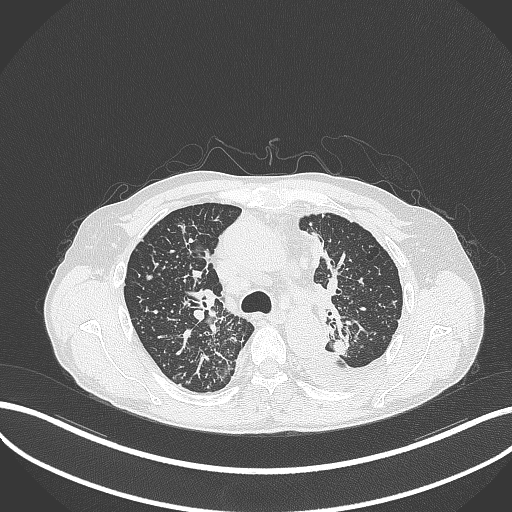
Chest CT, one axial slice. Position 248 of 325 along the scan axis. Reconstruction kernel B70f. Lung window (W 1500 / L -600 HU). 1 mm slice thickness. 512 × 512 image matrix. Patient: male, 58 years. From the clinical record (not read from this slice): clinical TNM (as recorded): T1c N3 M1.
Annotated regions visible in this slice (rectangle marked by the reading radiologist):
- lung tumour (recorded histology: adenocarcinoma): box from (x=330, y=332) to (x=351, y=357) px